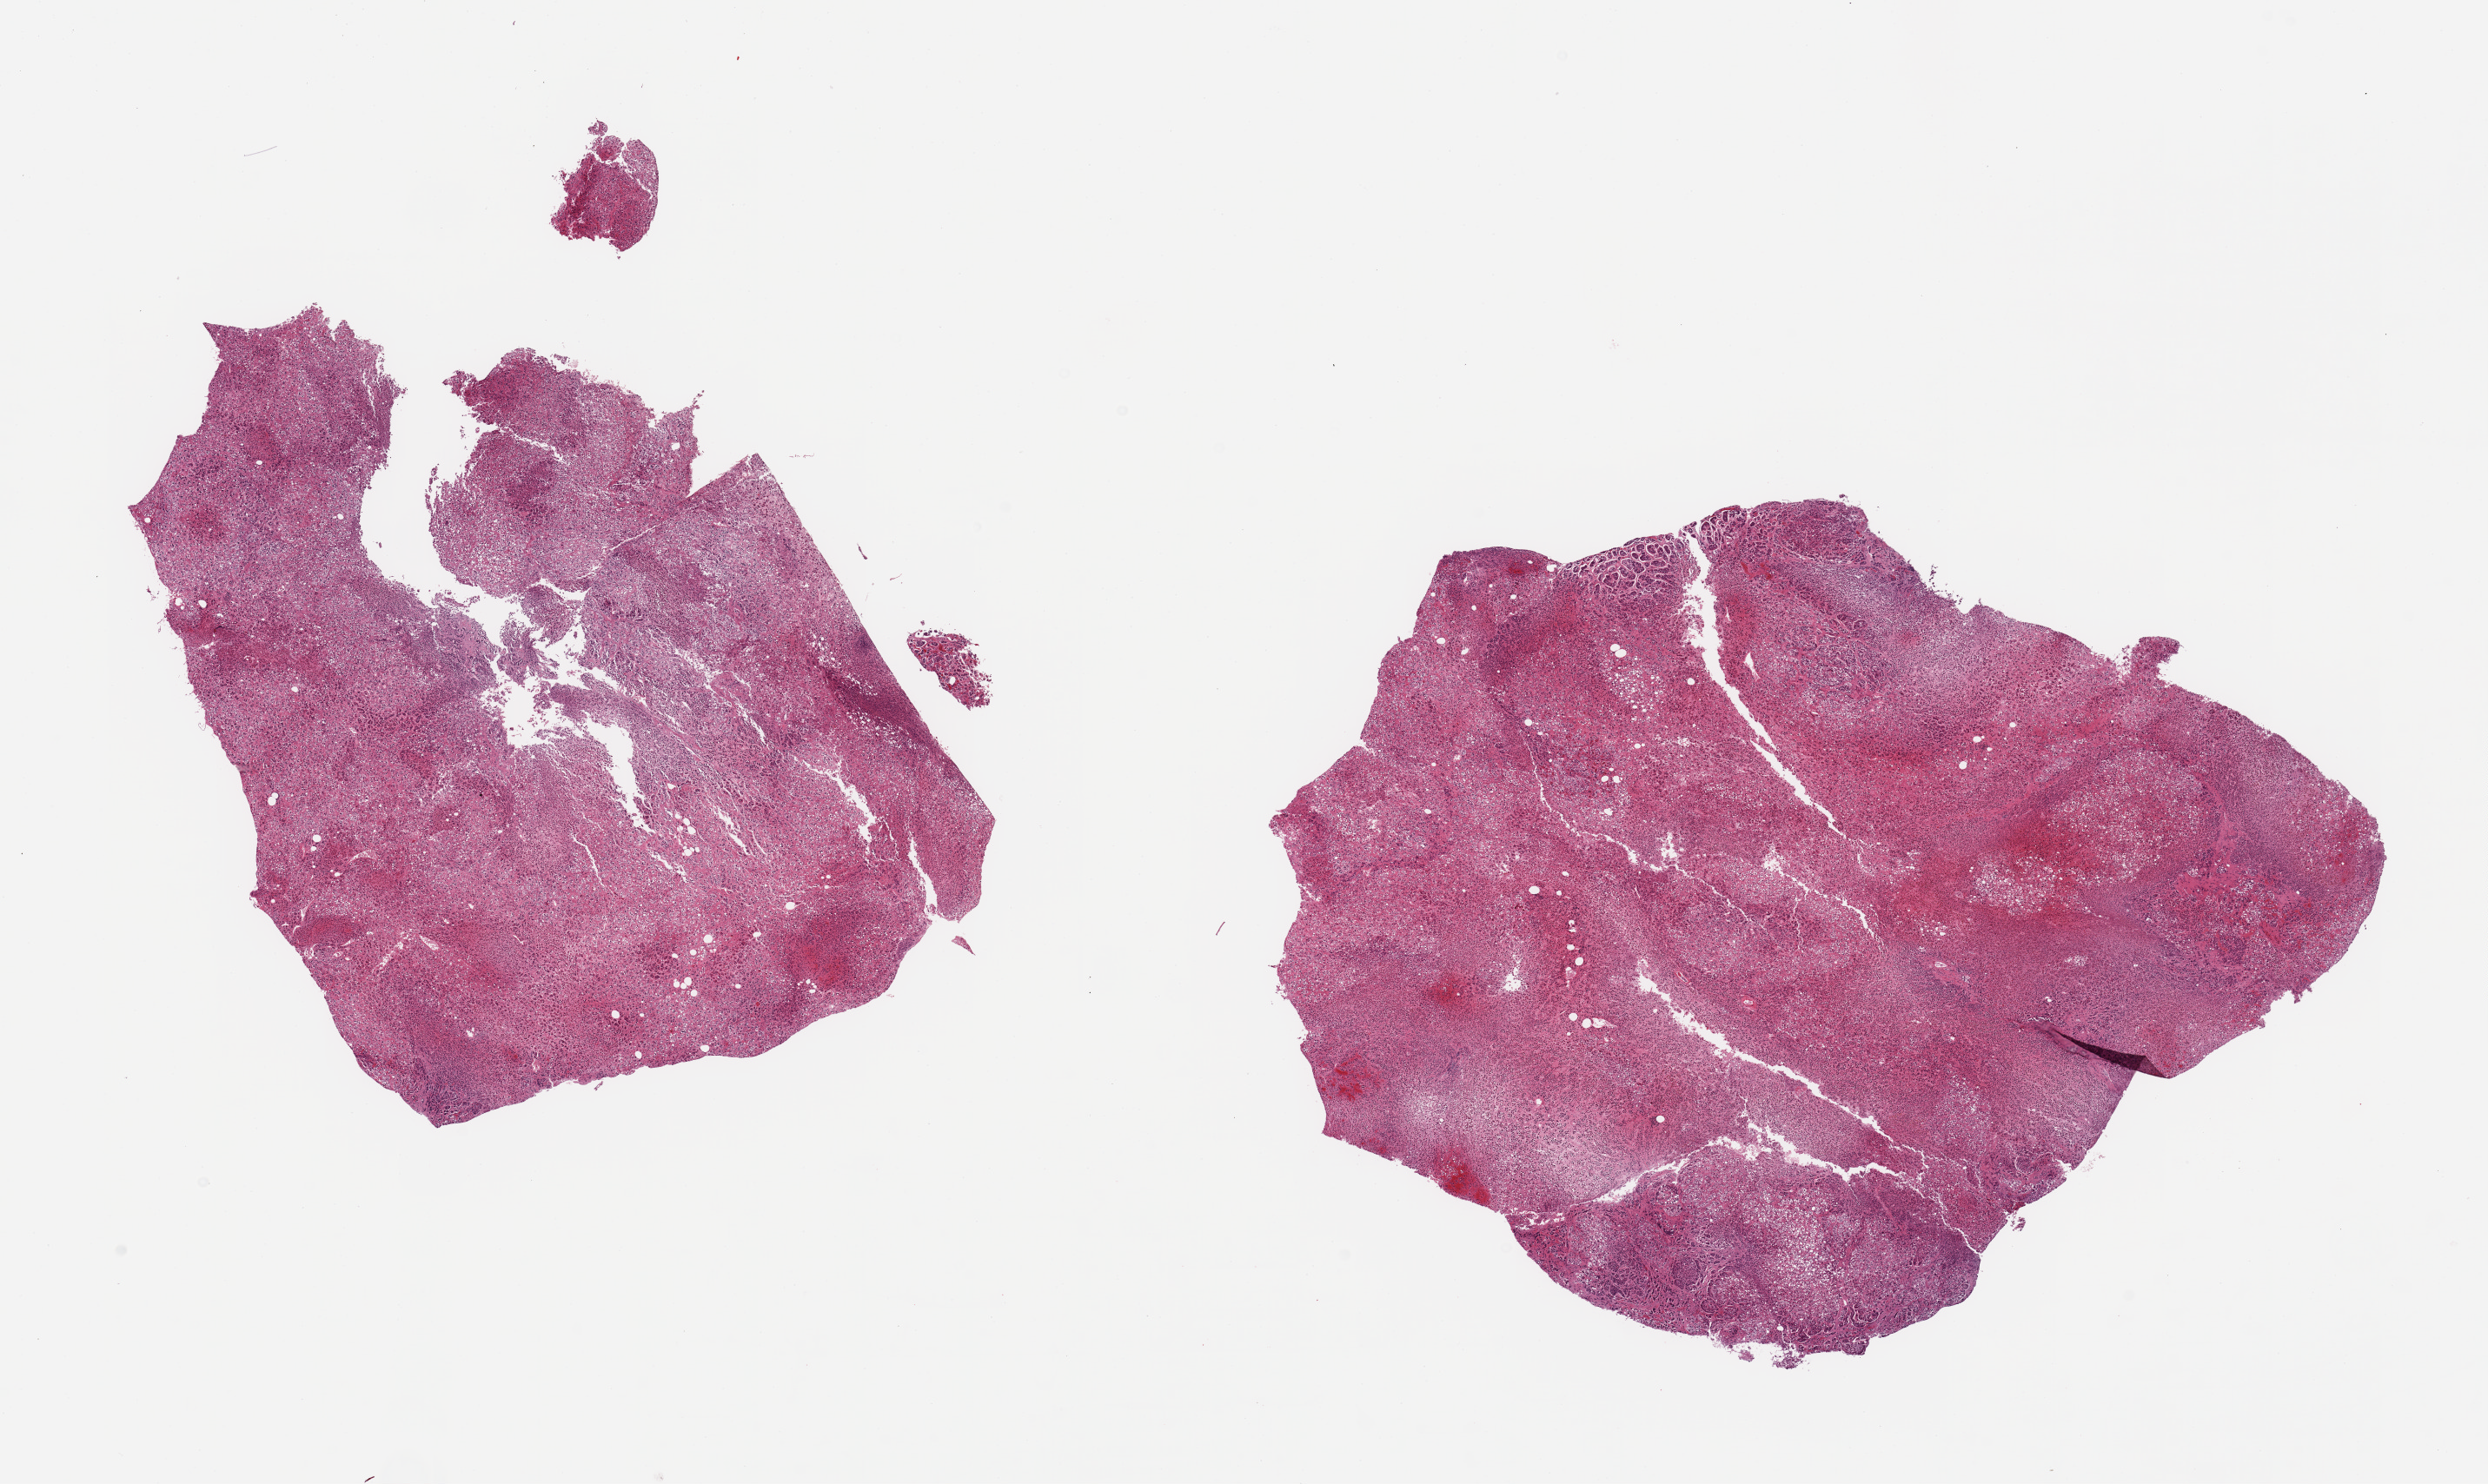
Whole-slide image, H&E stain — shown as a low-resolution overview of the whole scanned area (about 22.6 x 13.5 mm, from a 20x scan); PAXgene-fixed paraffin-embedded (PFPE) section; sampled site (target tissue): adrenal gland; donor tissue sample. Donor sex: male.
Review note (as recorded): 2 pieces; no fat but poorly preserved.